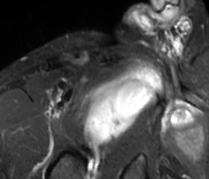
MRI of an extremity soft-tissue mass, one axial slice; STIR; MR volume resampled by the dataset authors to the PET/CT grid (not the native acquisition matrix); 3.27 mm slice thickness; 209 × 179 image matrix, field of view 204 × 175 mm. Male patient. From the clinical record (not read from this slice): histological type: undifferentiated - pleiomorphic; grade: high; site of the primary tumour: right thigh.
Annotated regions visible in this slice (expert contour drawn on MRI and transferred to this co-registered scan by the dataset authors):
- gross tumour volume including surrounding oedema: bounding box (x1, y1, x2, y2) in pixels: (82, 62, 161, 147)
- gross tumour volume (mass): (82, 69, 161, 145)